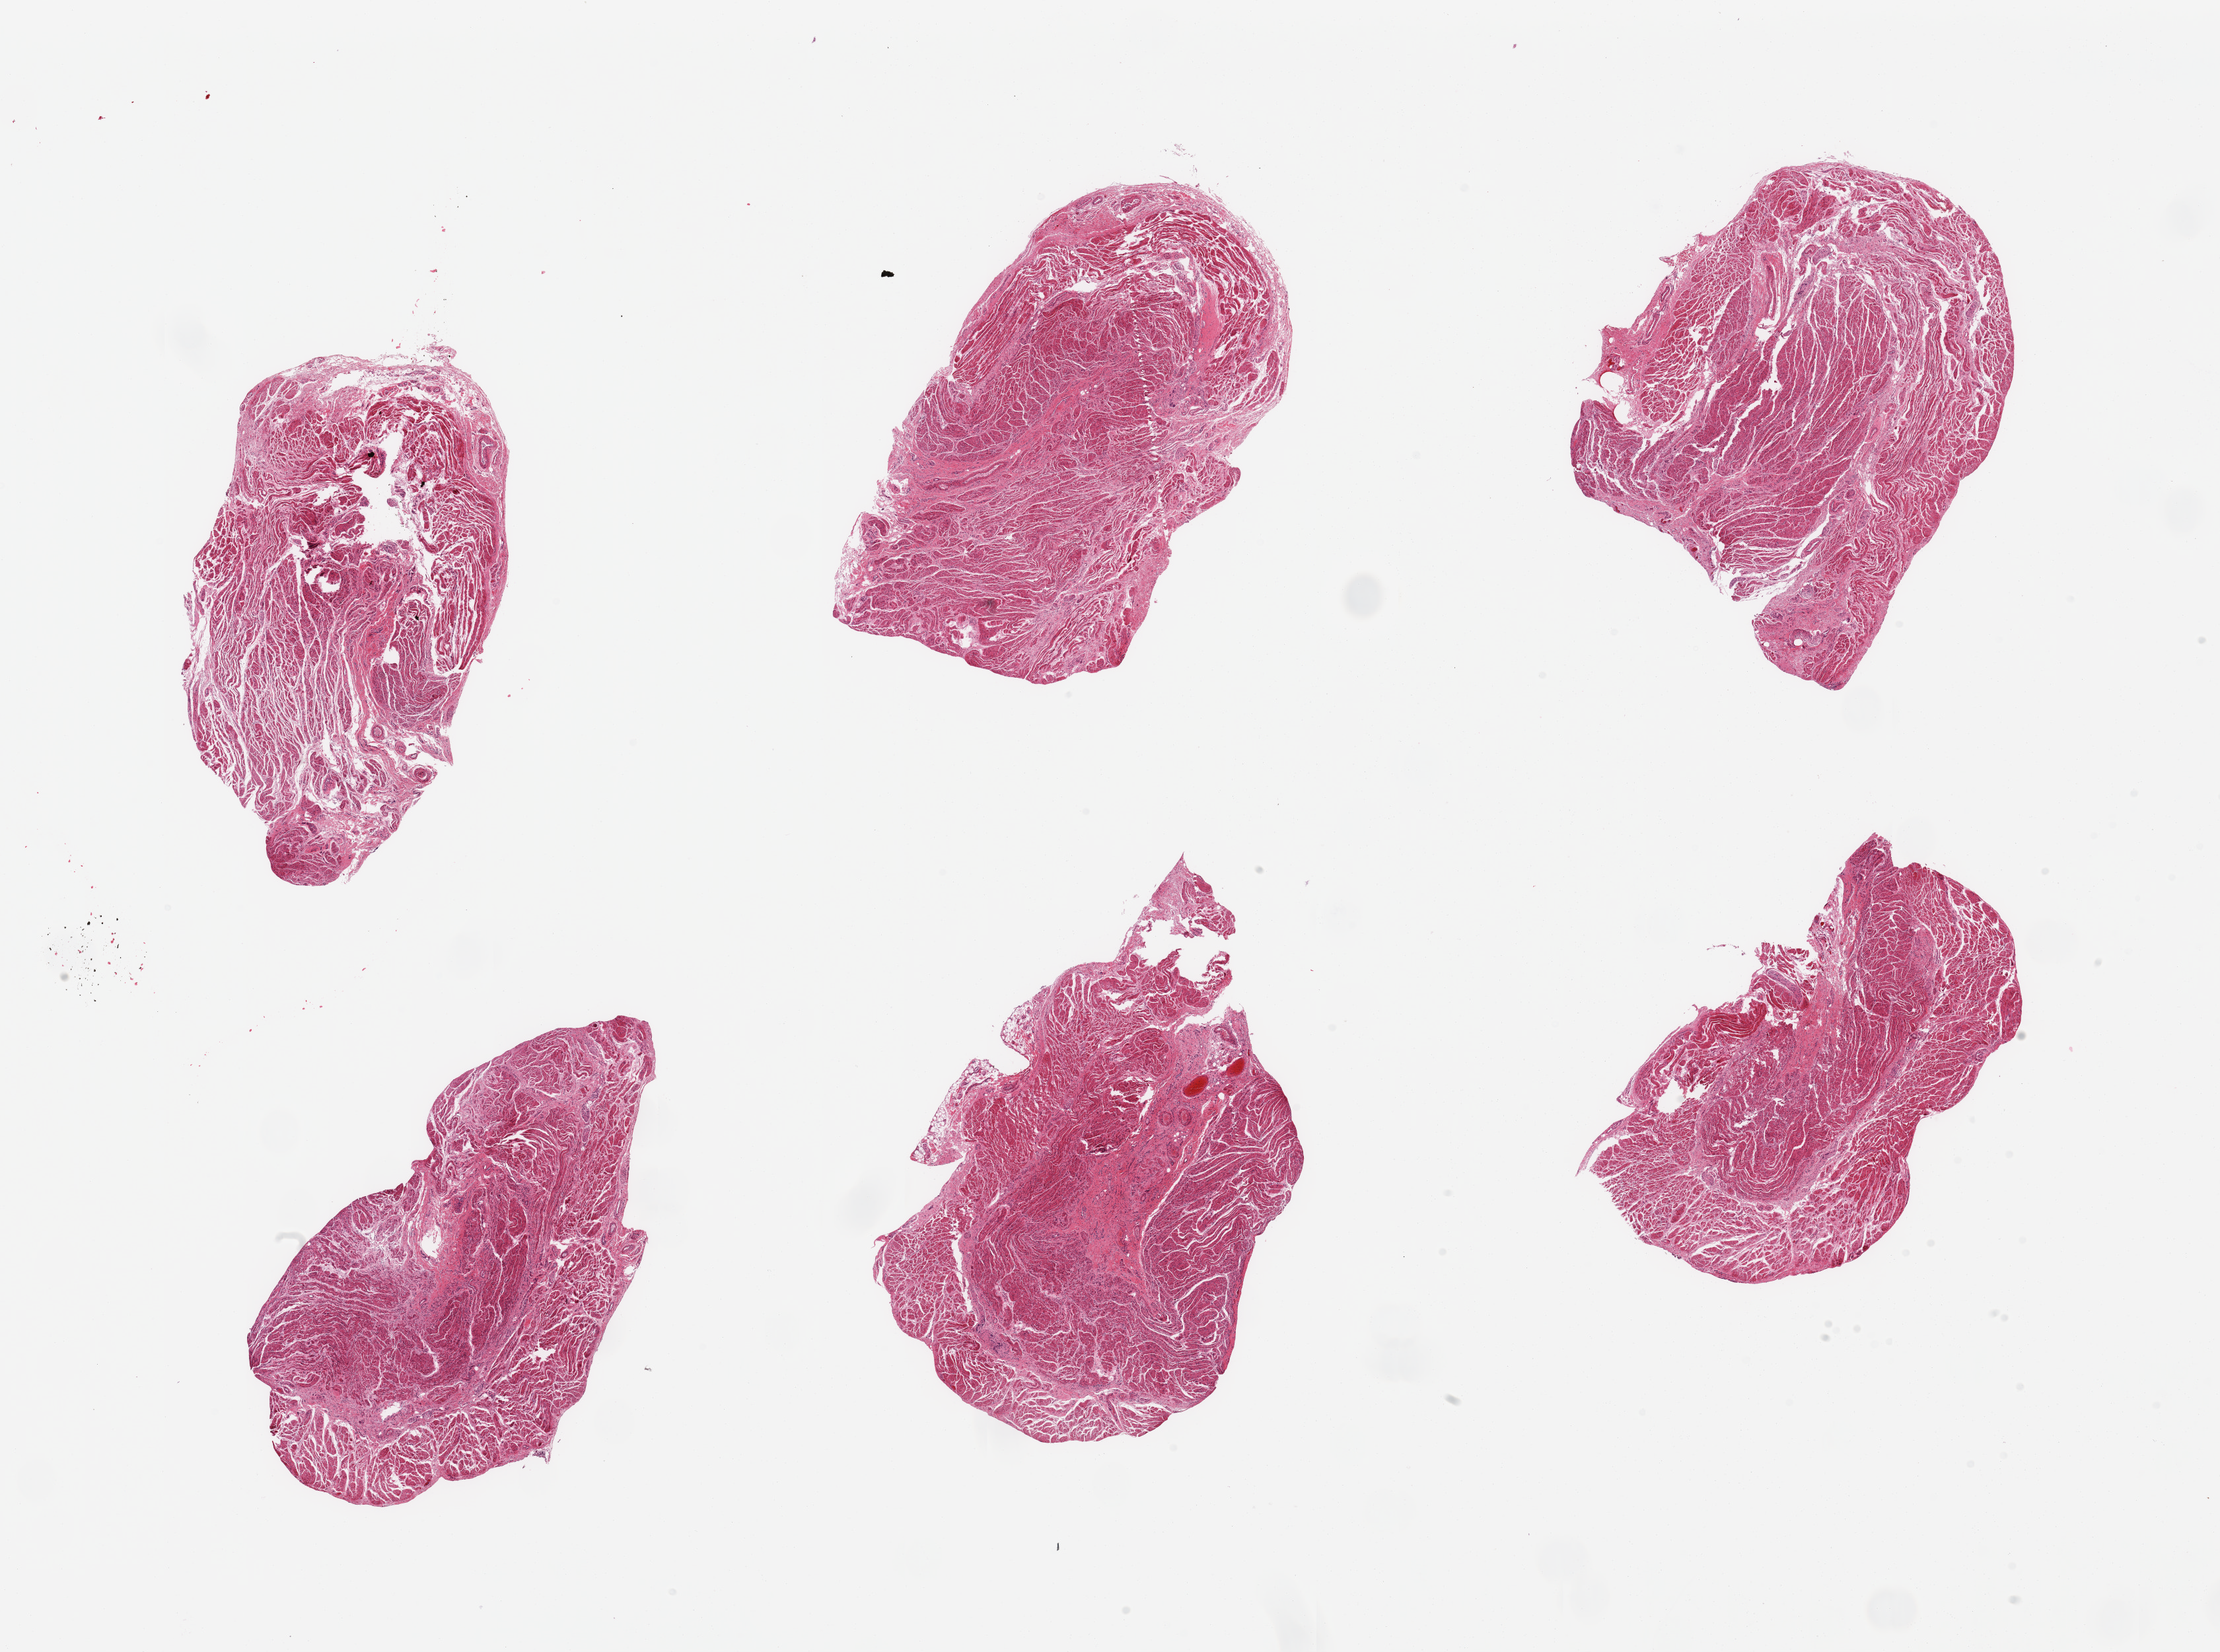
Whole-slide image, H&E stain — whole scanned area (about 26.6 x 19.8 mm) shown as a low-resolution overview. PAXgene-fixed, paraffin-embedded tissue. Section of gastroesophageal junction (target tissue). Donor tissue sample. Female donor.
Reviewer comment on this tissue sample: 6 pieces, confirmed target muscularis.